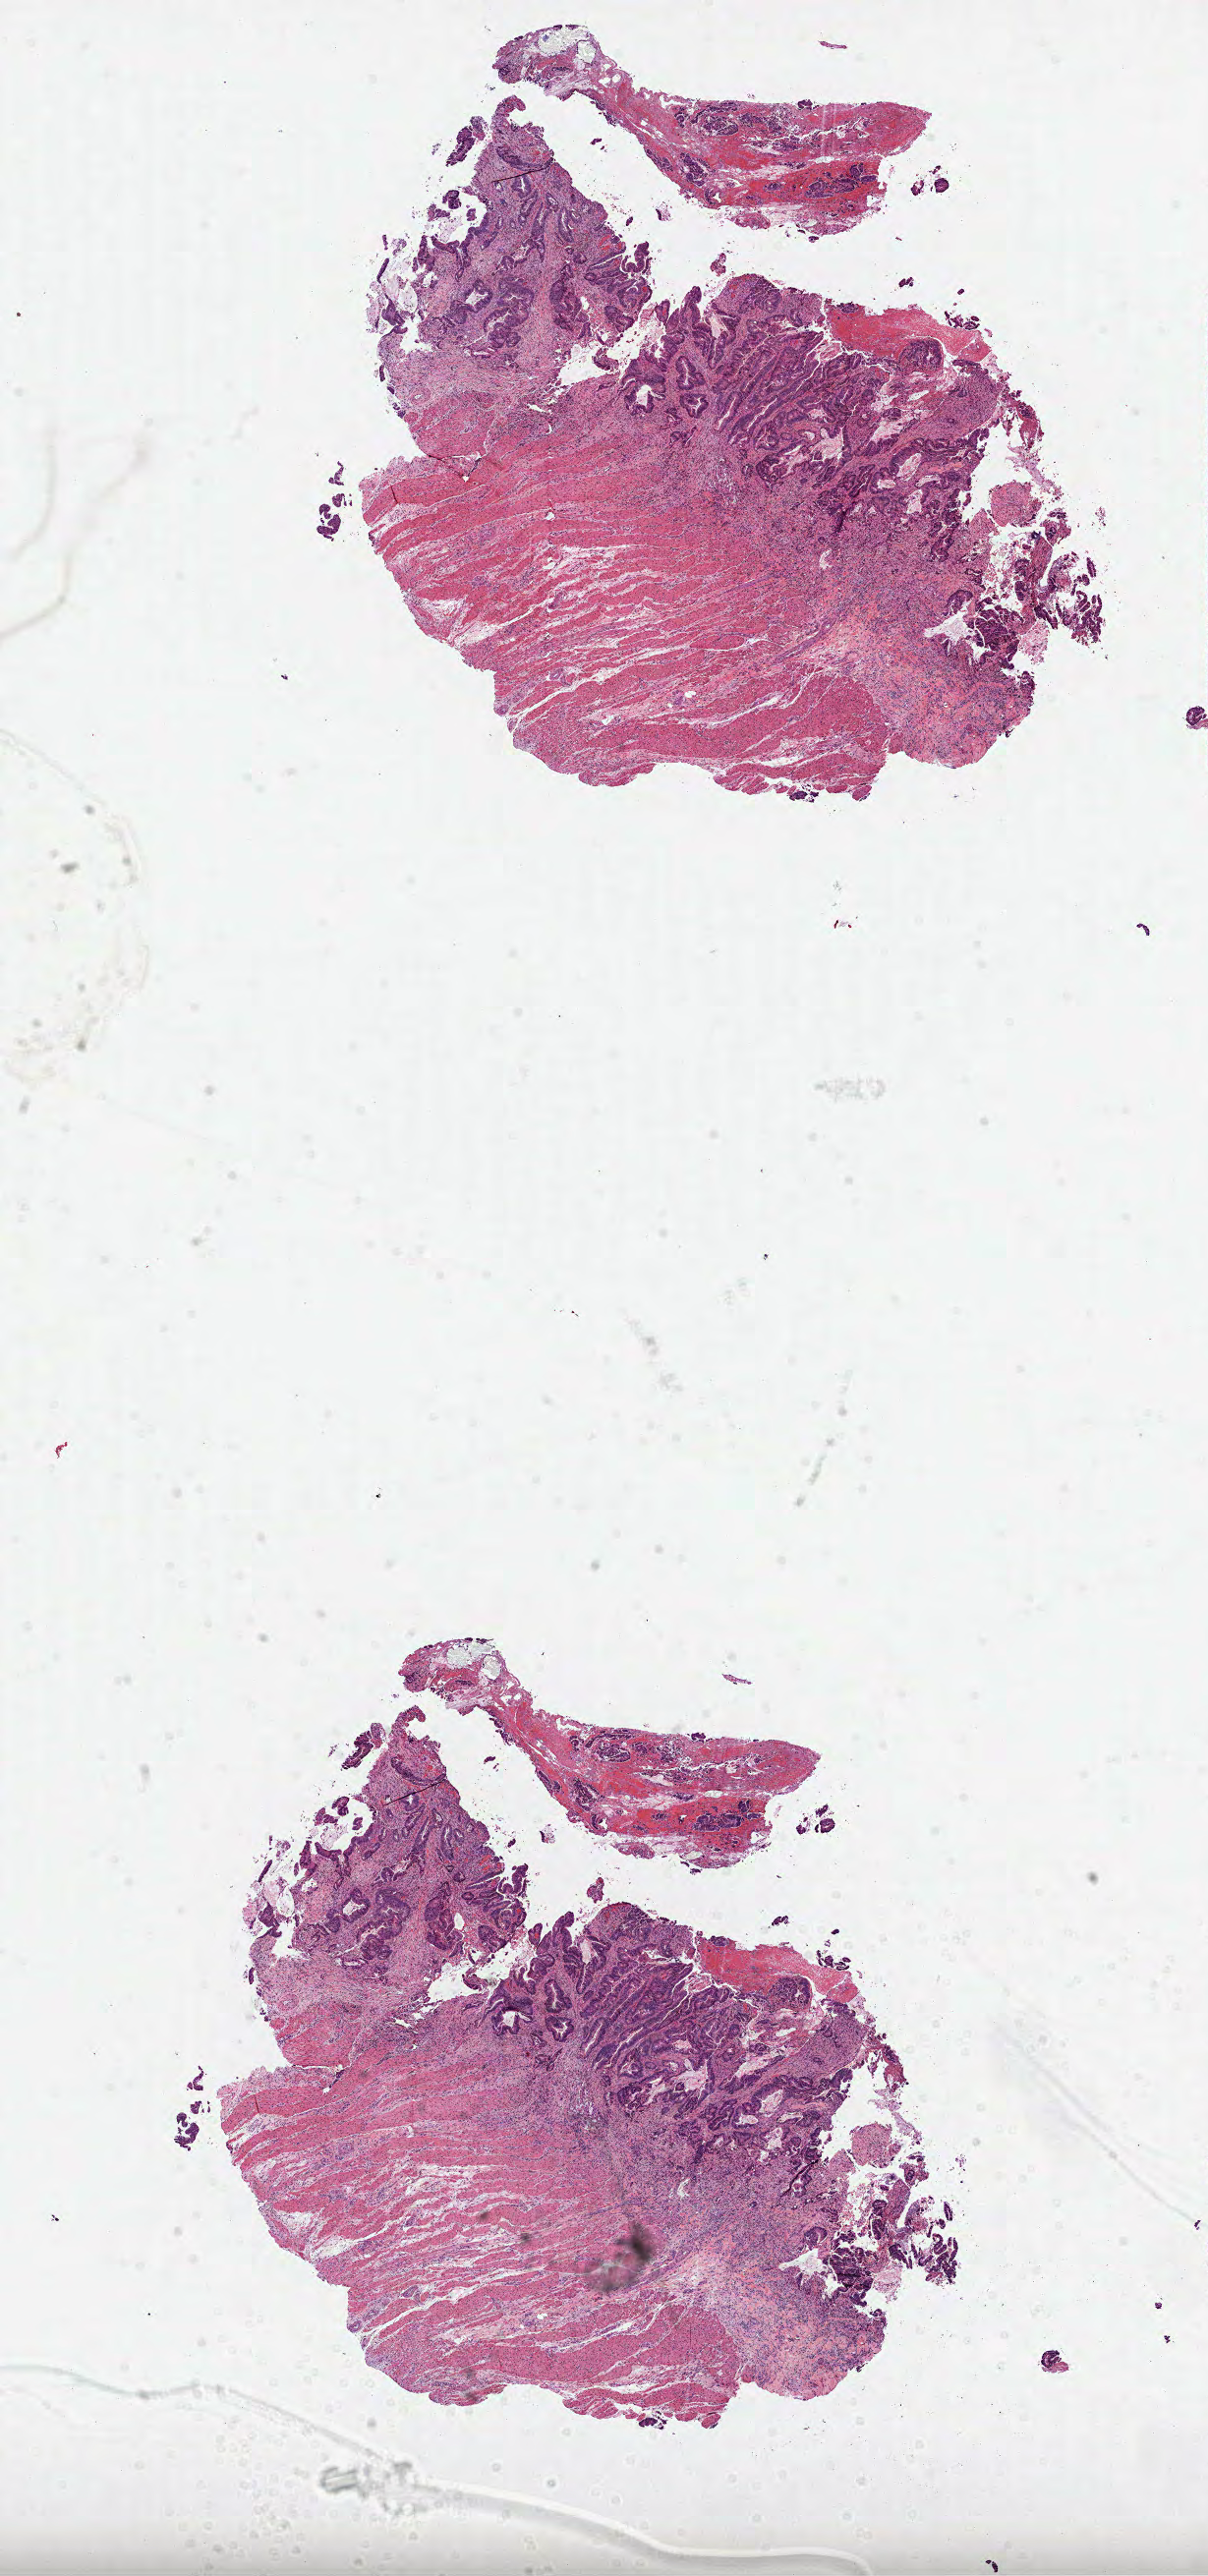
Digitized Hematoxylin and eosin (H&E) stained tissue section (whole slide), a low-resolution overview of the entire scanned area, about 9.9 x 21.1 mm; formalin-fixed paraffin-embedded (FFPE) diagnostic section; sample: primary tumour, colon. Female patient; age at initial diagnosis 73 years.
Diagnosis: Adenocarcinoma, NOS. AJCC pathologic stage: IIA.